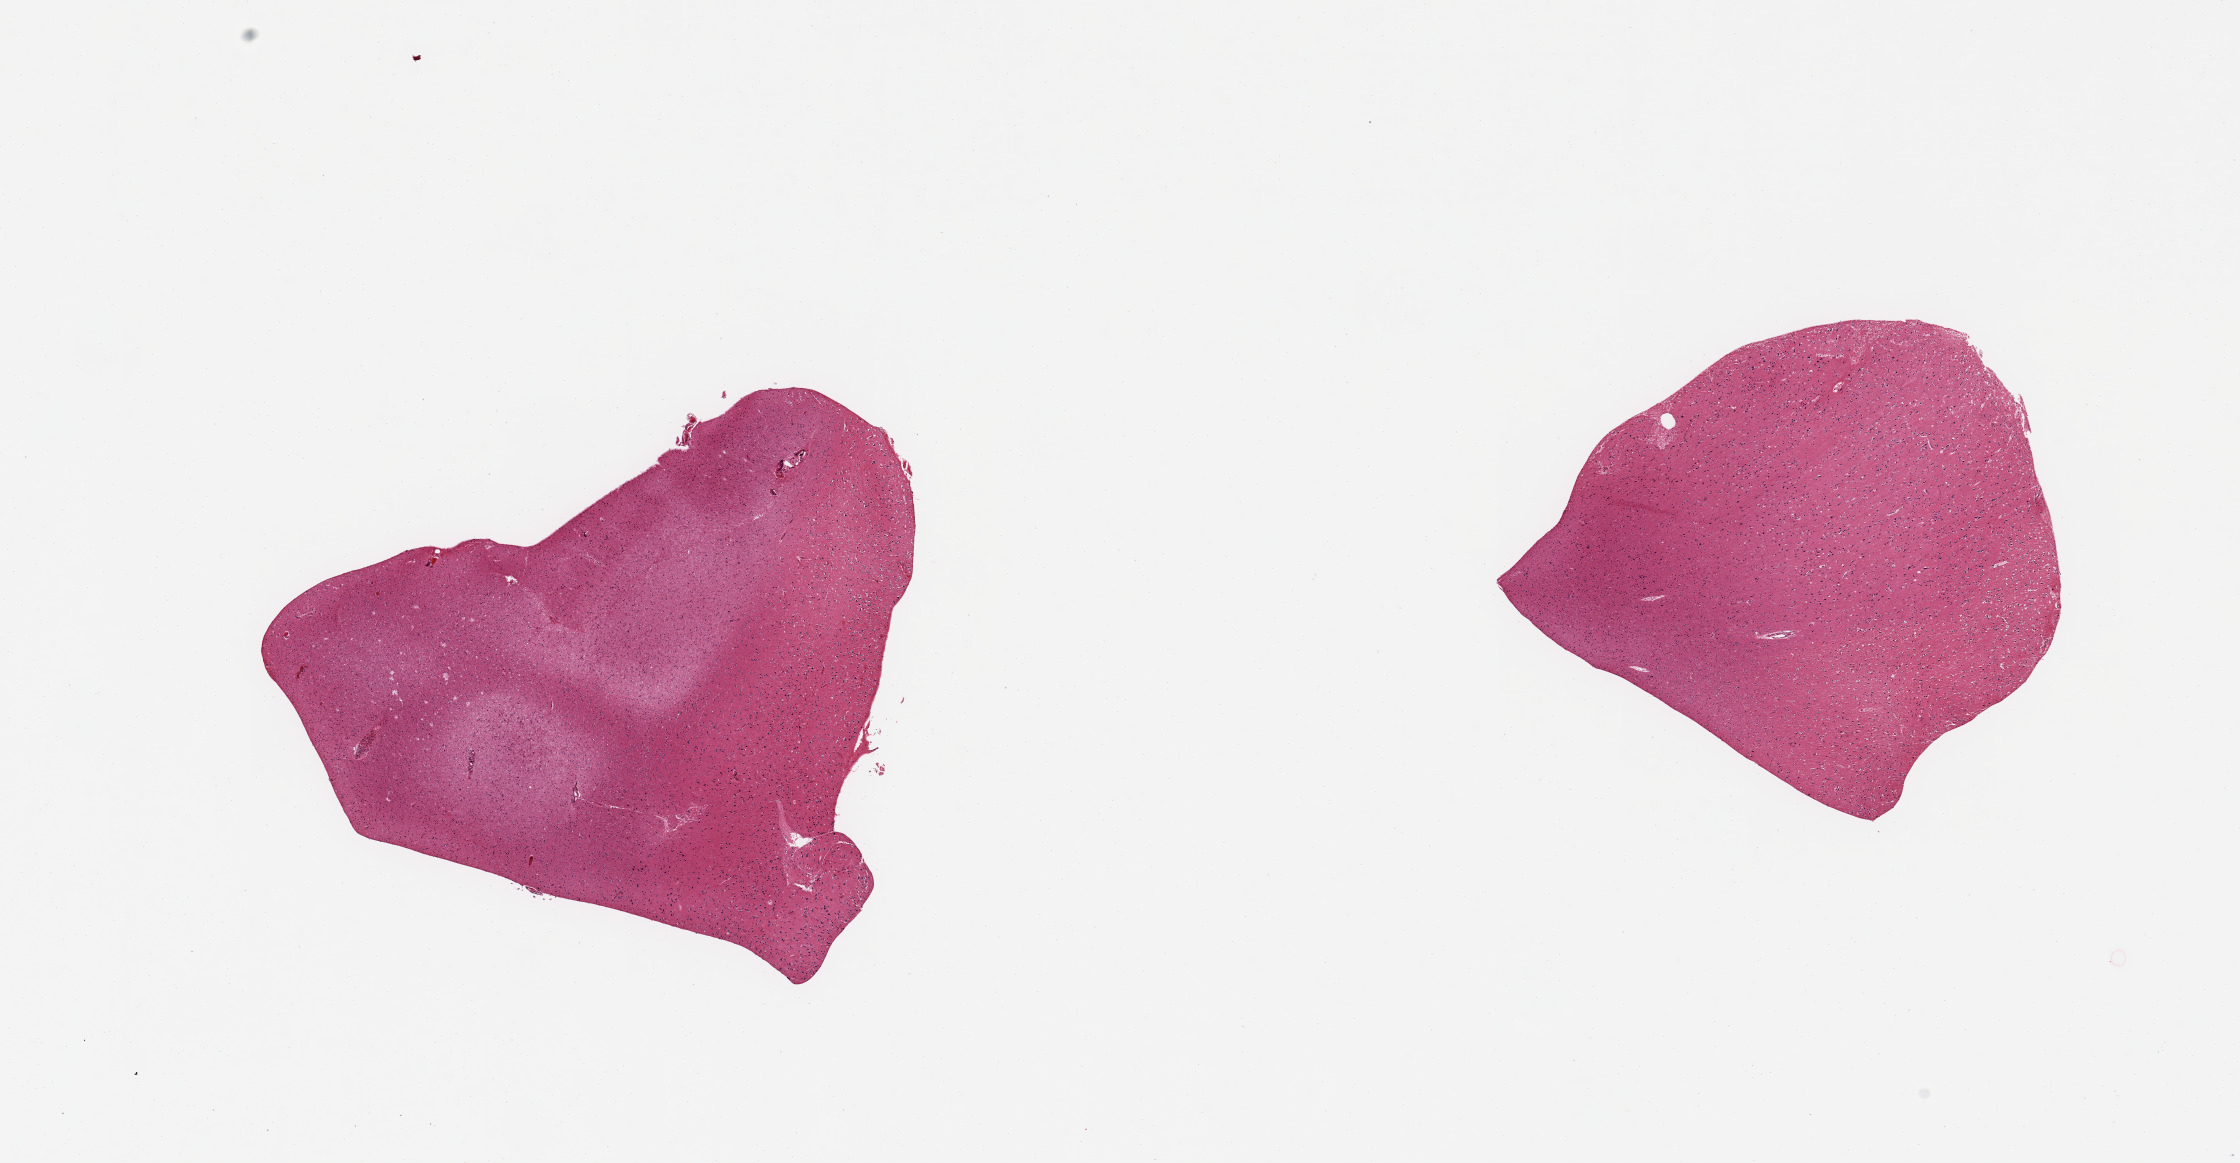
Whole-slide image, haematoxylin and eosin stain — a low-resolution overview of the entire scanned area, about 17.7 x 9.2 mm; PAXgene-fixed paraffin-embedded (PFPE) section; target tissue: cerebral cortex; donor tissue sample. Donor sex: male.
Review note (as recorded): 2 pieces; some admixture with white matter.